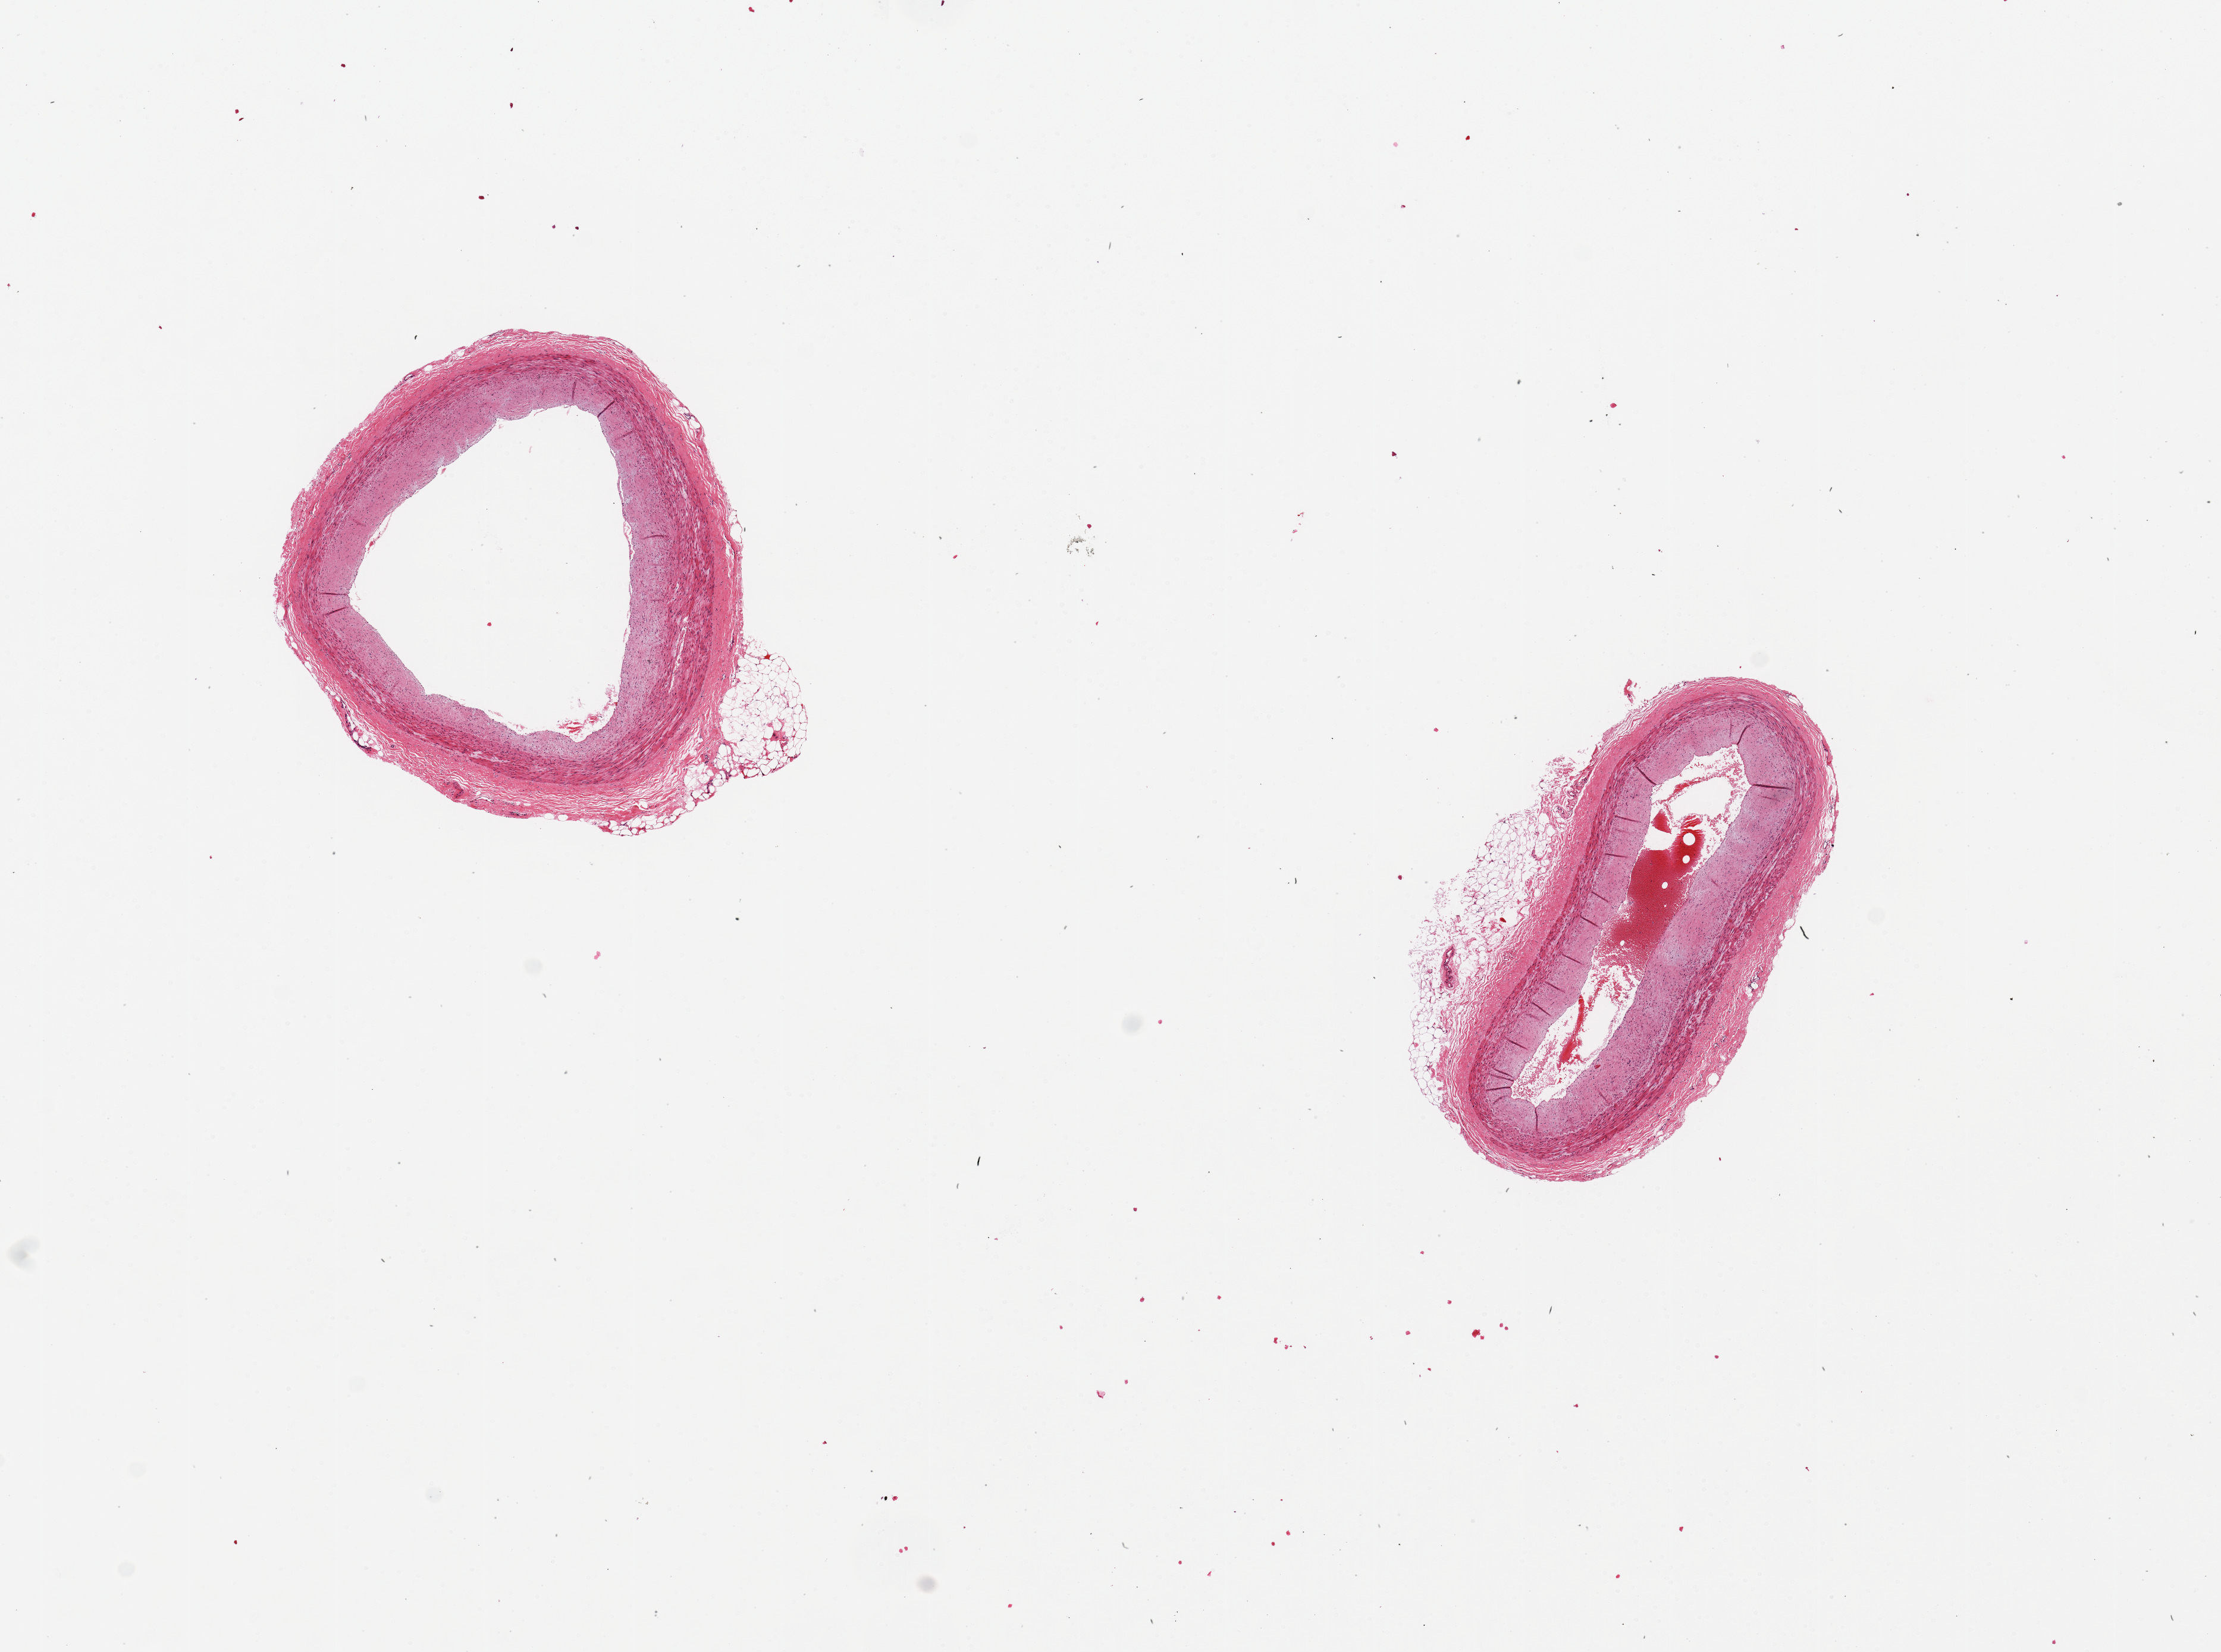
Haematoxylin and eosin whole-slide image, low-resolution overview of the scanned area, about 14.8 x 11.0 mm (slide scanned at 20x), PAXgene-fixed paraffin-embedded (PFPE) section, target tissue: coronary artery, donor tissue sample. Male donor.
- review note (as recorded): 2 pieces ~2mm d. Minimal atherosclerosis